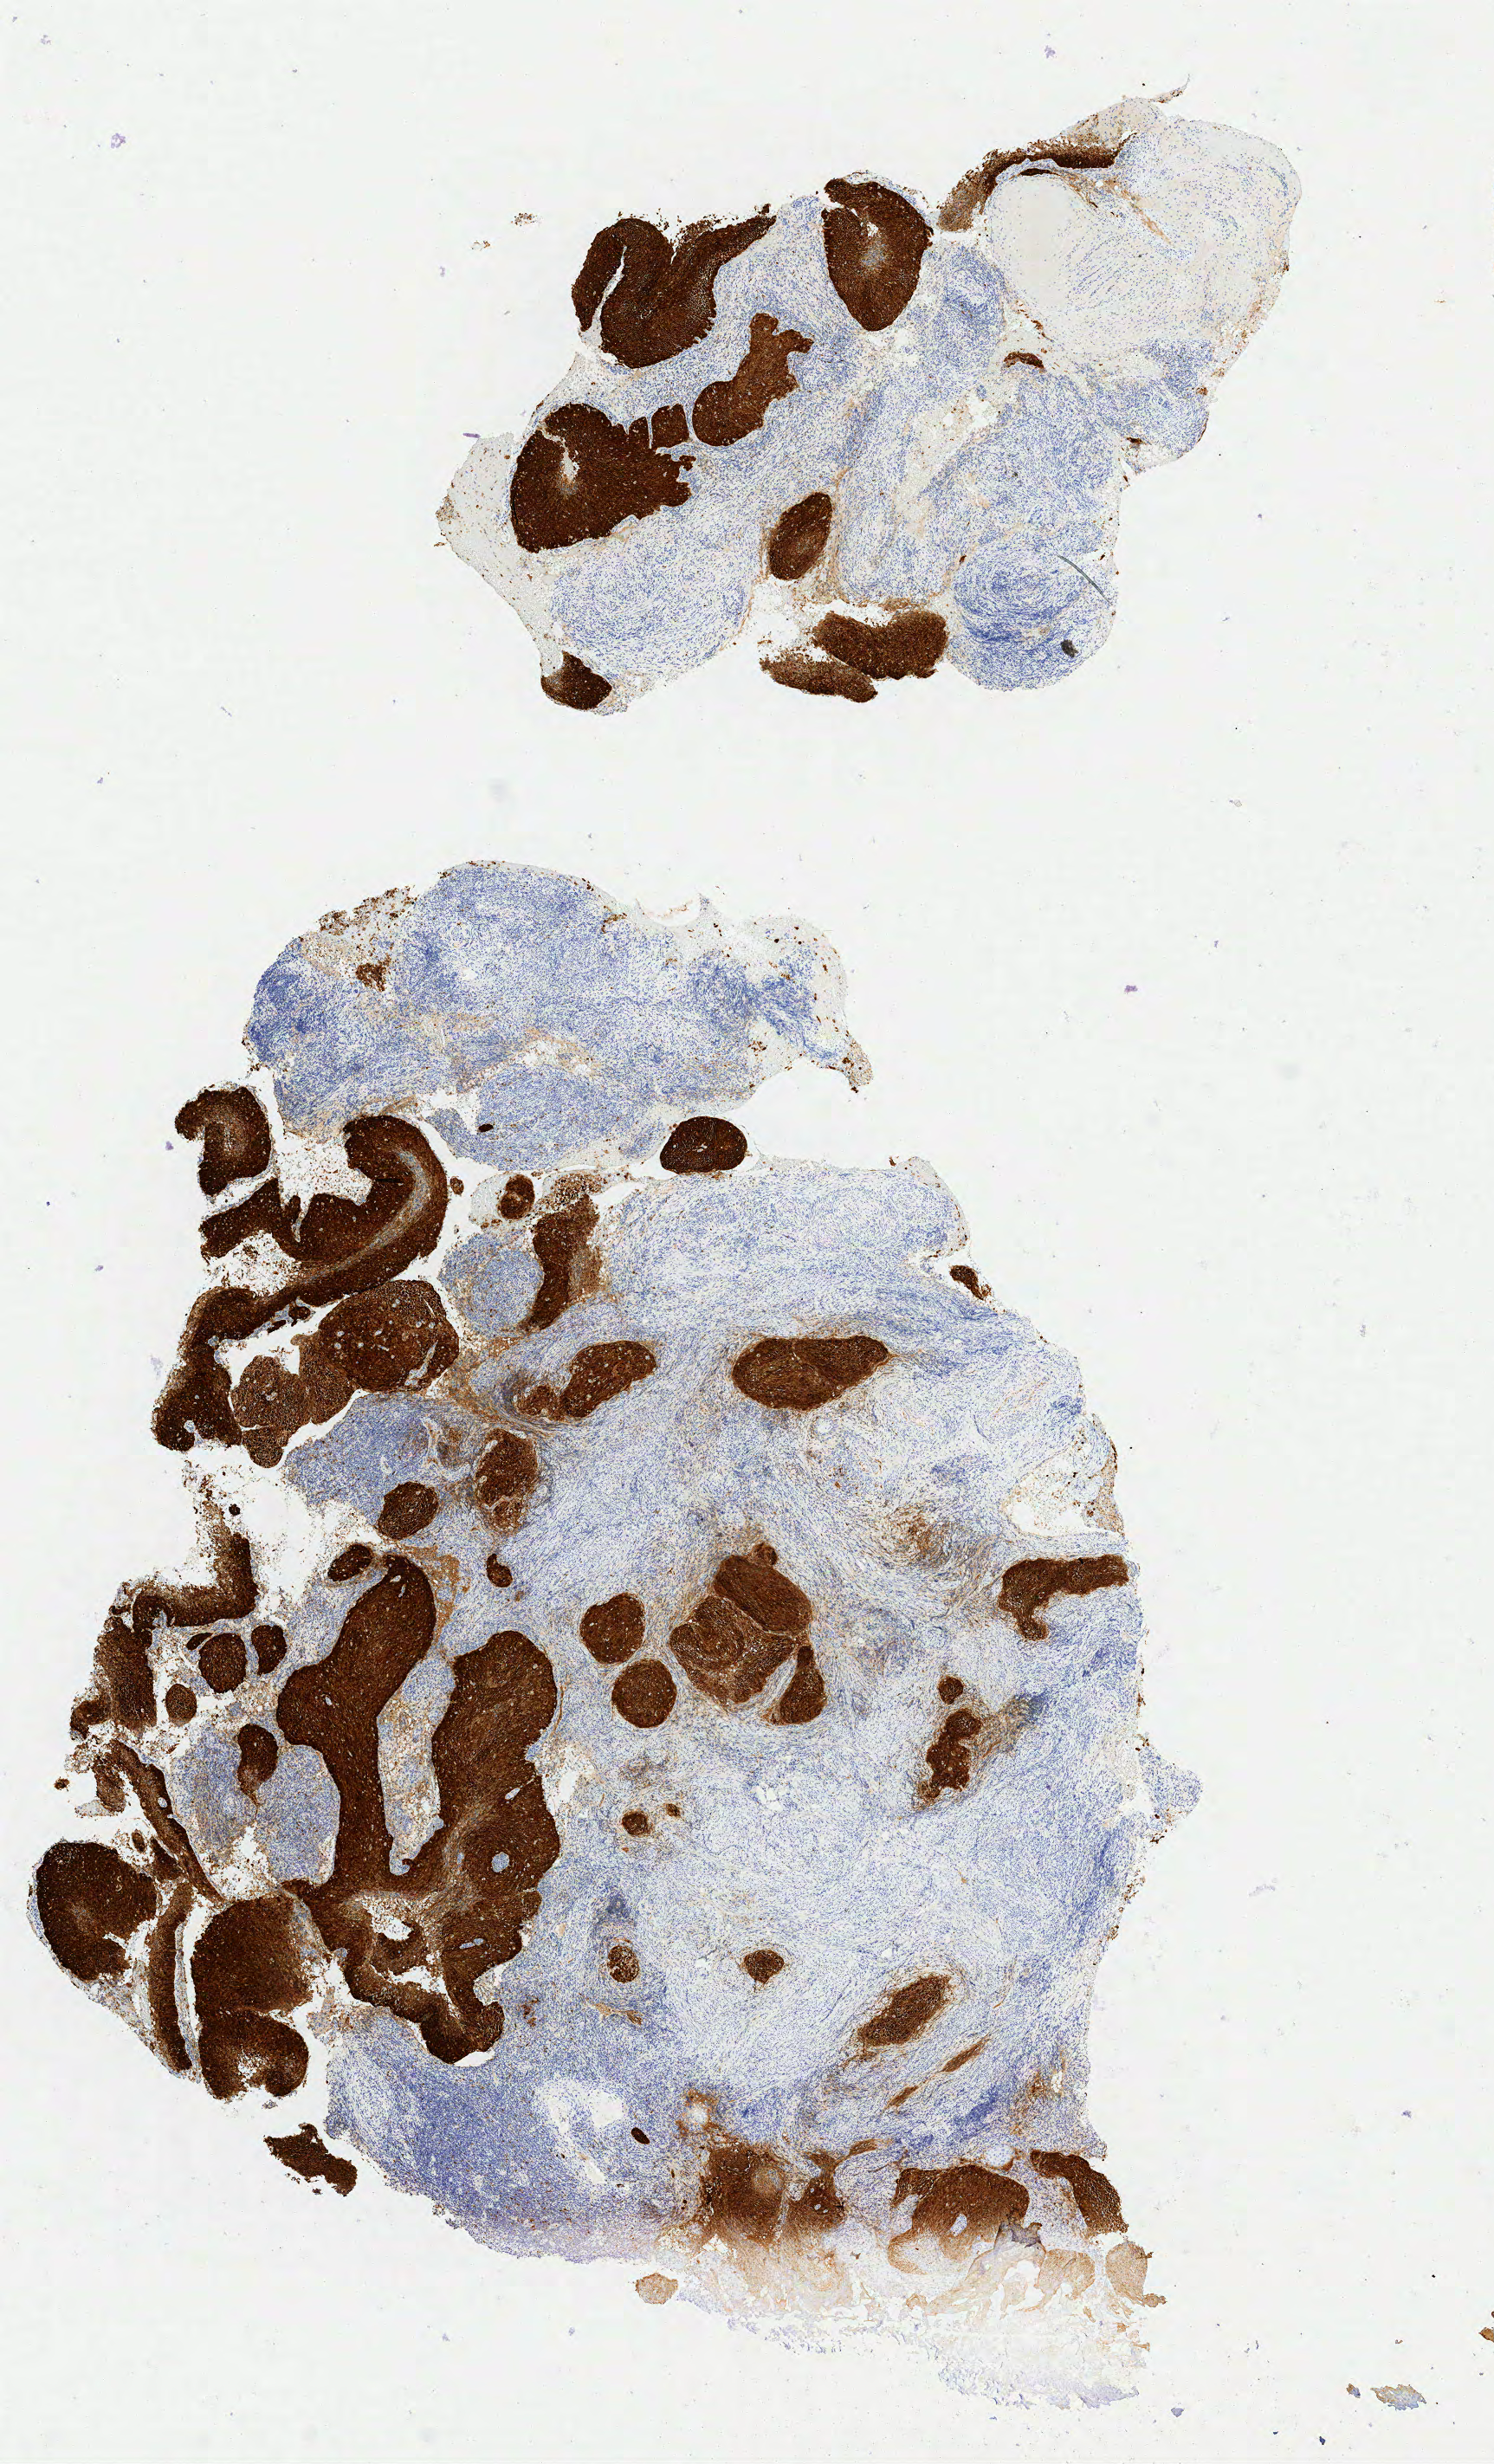
Immunohistochemistry (IHC) whole-slide image stained for p16 (p16INK4a) — a low-resolution overview of the entire scanned area, about 6.9 x 11.3 mm; tumor tissue; site: cervix. Patient: female, aged 54.
* diagnosis: Squamous cell carcinoma, large cell, nonkeratinizing, NOS